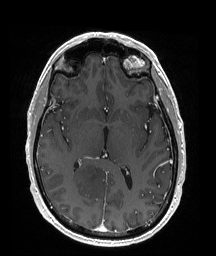
Brain MRI from a brain-tumour surgery series, one axial slice; slice 95 of 176 in the series (ordered by position); T1-weighted post-contrast; 1 mm slice thickness; 216 × 256 image matrix, field of view 211 × 250 mm. From the clinical record (not read from this slice): histopathology: Oligodendroglioma; WHO grade: 2; IDH mutation: yes; tumour location: Right Parietal.
Structures marked on this image (expert manual segmentation):
- tumour: bounding box [x1, y1, x2, y2] px = [70, 159, 111, 197]